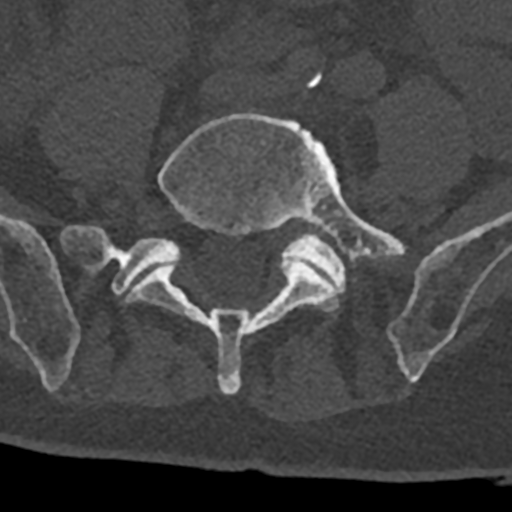
CT including the spine, one axial slice; position 191 of 797 along the scan axis; 120 kVp; bone window (W 1800 / L 400 HU); 512 × 512 image matrix. Patient: male, 74 years. From the clinical record (not read from this slice): primary cancer: renal.
Structures marked on this image (semi-automatic segmentation, software-assisted and operator-edited):
- L5 vertebra: bounding box (x1, y1, x2, y2) in pixels: (126, 113, 405, 394)